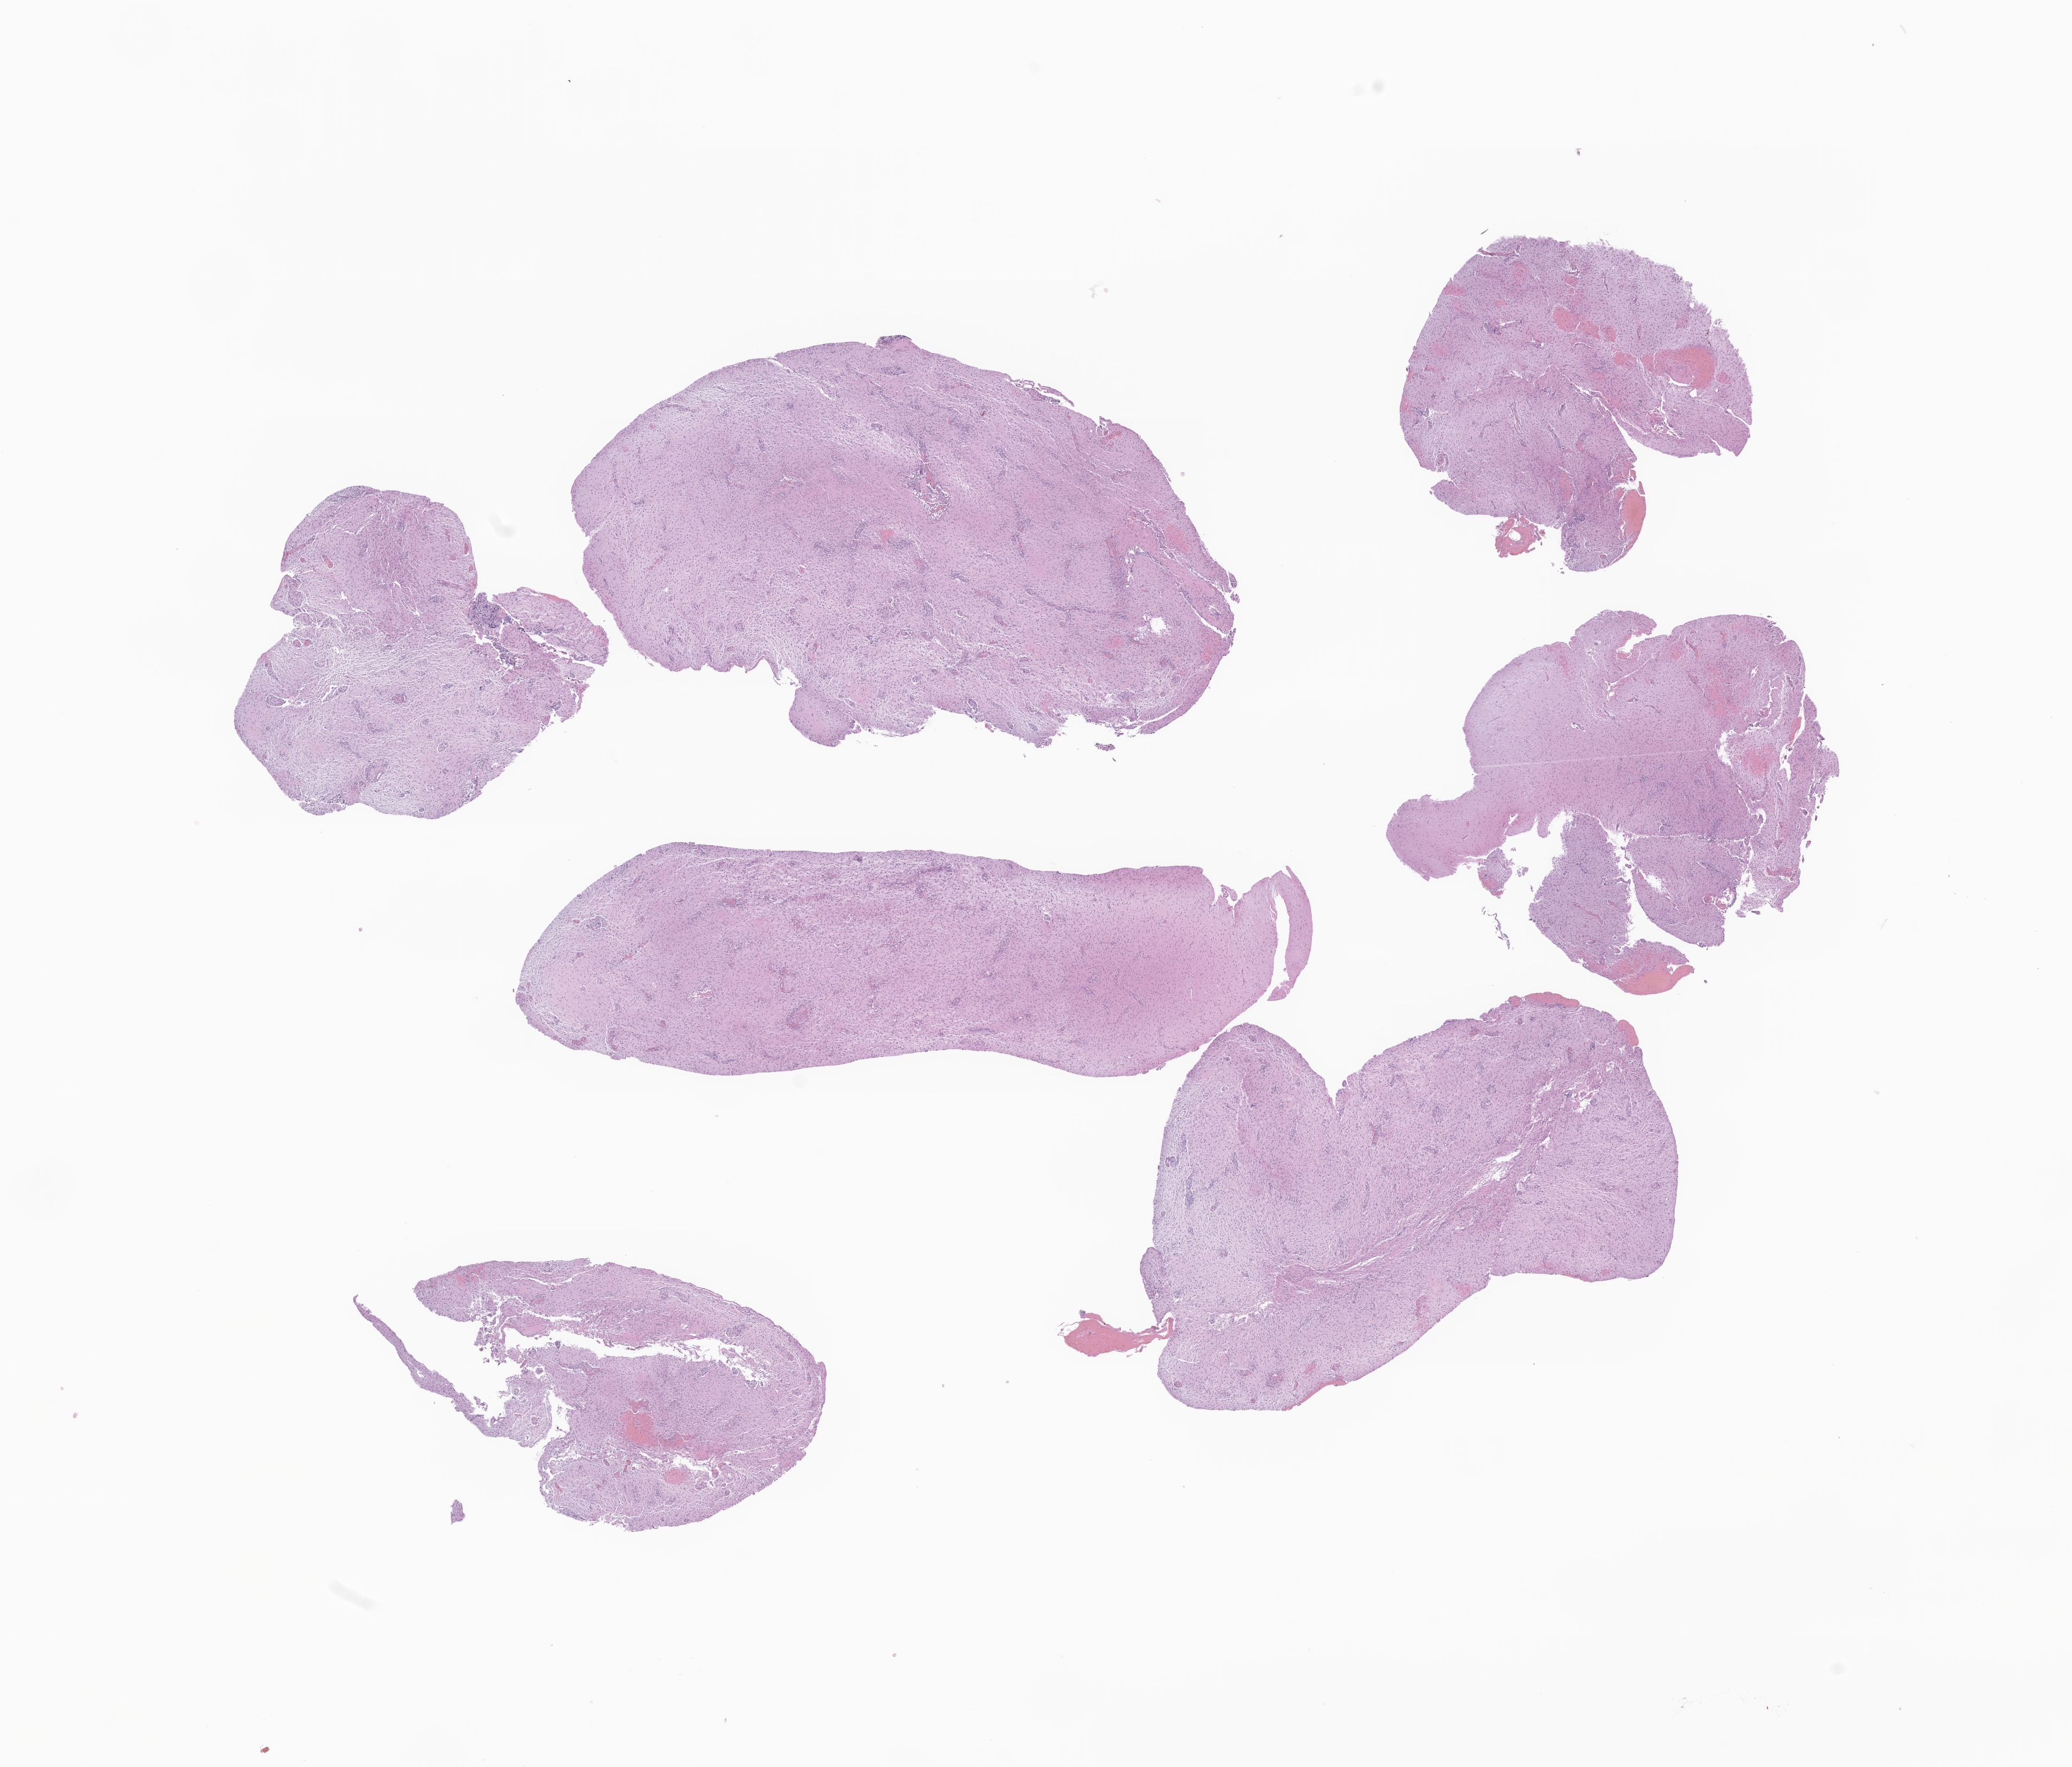
Digitized H&E-stained section of tumor tissue from the cerebellum — whole scanned area (about 16.3 x 13.9 mm) shown as a low-resolution overview, formalin-fixed paraffin-embedded section. Patient: female, age 117 months (9 years 9 months).
- recorded diagnosis: Pilocytic astrocytoma